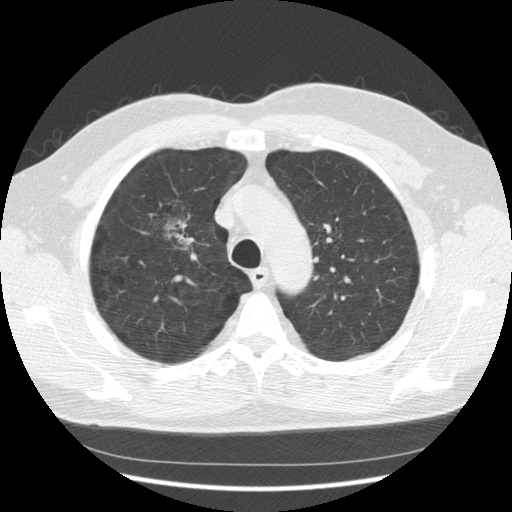
Low-dose screening chest CT, one axial slice; slice 94 of 133 in the series (ordered by position); reconstruction kernel STANDARD; 140 kVp; lung window (W 1500 / L -600 HU); 2.5 mm slice thickness; 512 × 512 image matrix.
Annotated regions visible in this slice (manually delineated by an expert):
- lesion 1 (tumor, upper lobe of right lung): bounding box (x1, y1, x2, y2) in pixels: (165, 219, 188, 250)